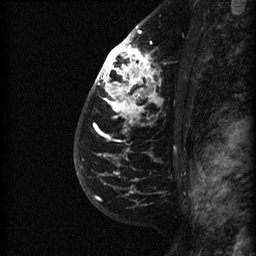
Breast MRI (dynamic contrast-enhanced), one sagittal slice. Slice 46 of 60 in the series (ordered by position). Dynamic contrast-enhanced series, image 2 of 3 at this slice position (ordered by acquisition). 1.5 T. TE 4.2 ms, TR 22.7 ms. 1.5 mm slice thickness. 256 × 256 image matrix. Female patient, age 48 years. Case-level facts recorded for this patient, not image findings: setting: breast cancer imaged before/during neoadjuvant chemotherapy; receptor status: triple-negative.
Outlined on this slice (semi-automatic segmentation, software-assisted and operator-edited):
- analysis volume of interest (the breast-tissue region the enhancement analysis was run in; not a lesion): bounding box (x1, y1, x2, y2) in pixels: (89, 27, 184, 180)
- tumour enhancement mask (voxels above the 90 % enhancement threshold inside the analysis volume of interest): (96, 31, 157, 157)